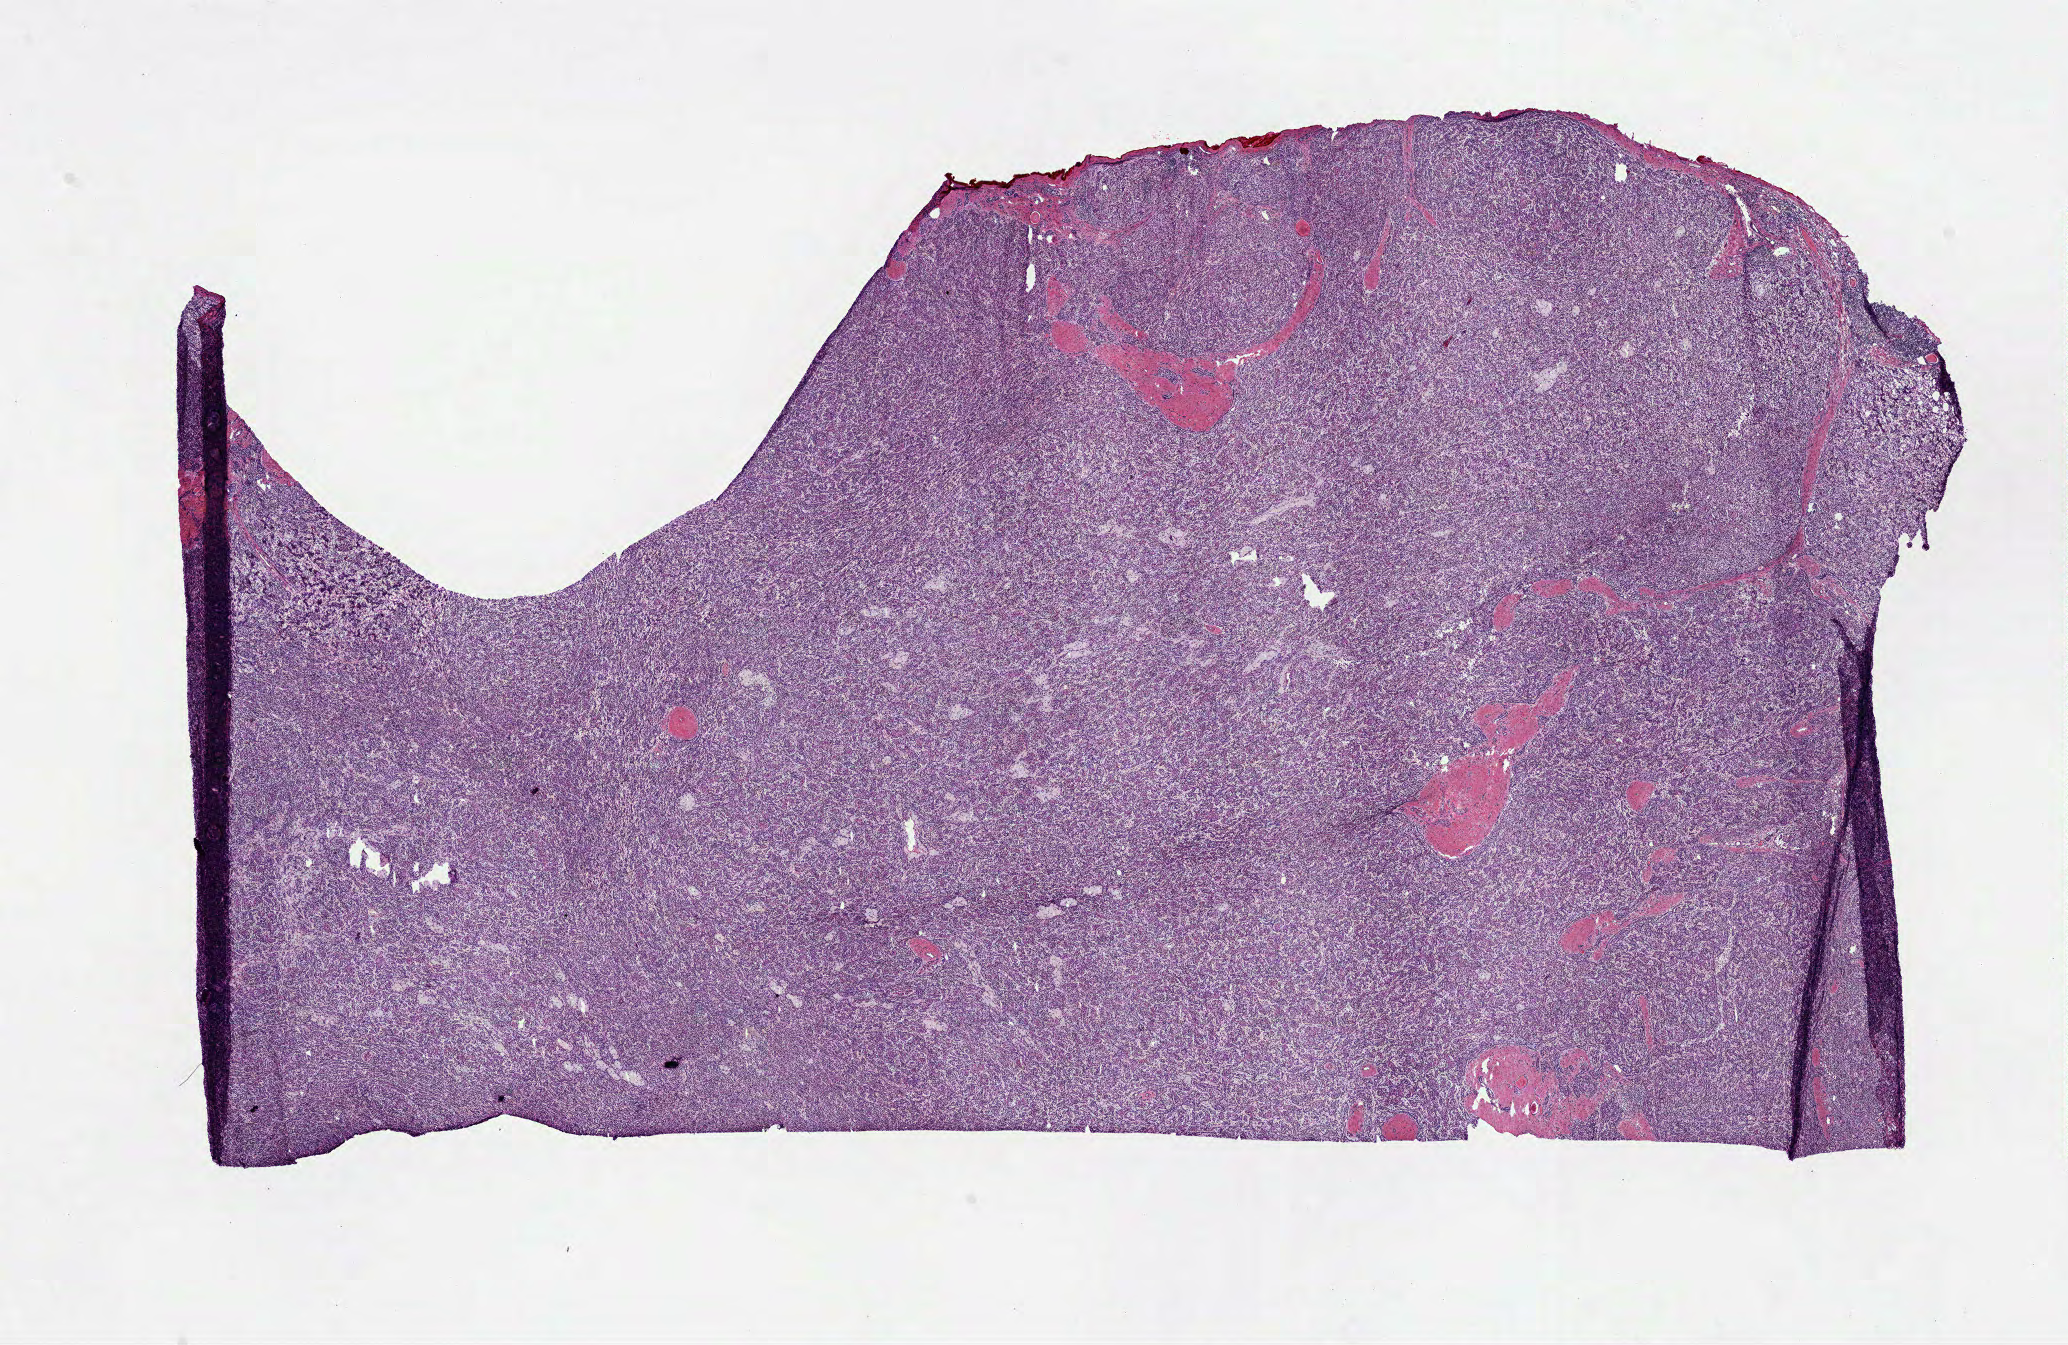
Whole-slide histology image, Hematoxylin and eosin (H&E) stained — low-resolution overview of the scanned area, about 16.7 x 10.8 mm (acquisition: 40x scan). Frozen section. Primary tumour sample from the kidney. Female, age 47 years at initial diagnosis. Slide review estimates, as recorded: tumour cells 95%, tumour nuclei 80%, normal cells 0%, stromal cells 5%, necrosis 0%.
Pathologic diagnosis: Papillary adenocarcinoma, NOS. AJCC pathologic stage: I (7th edition).